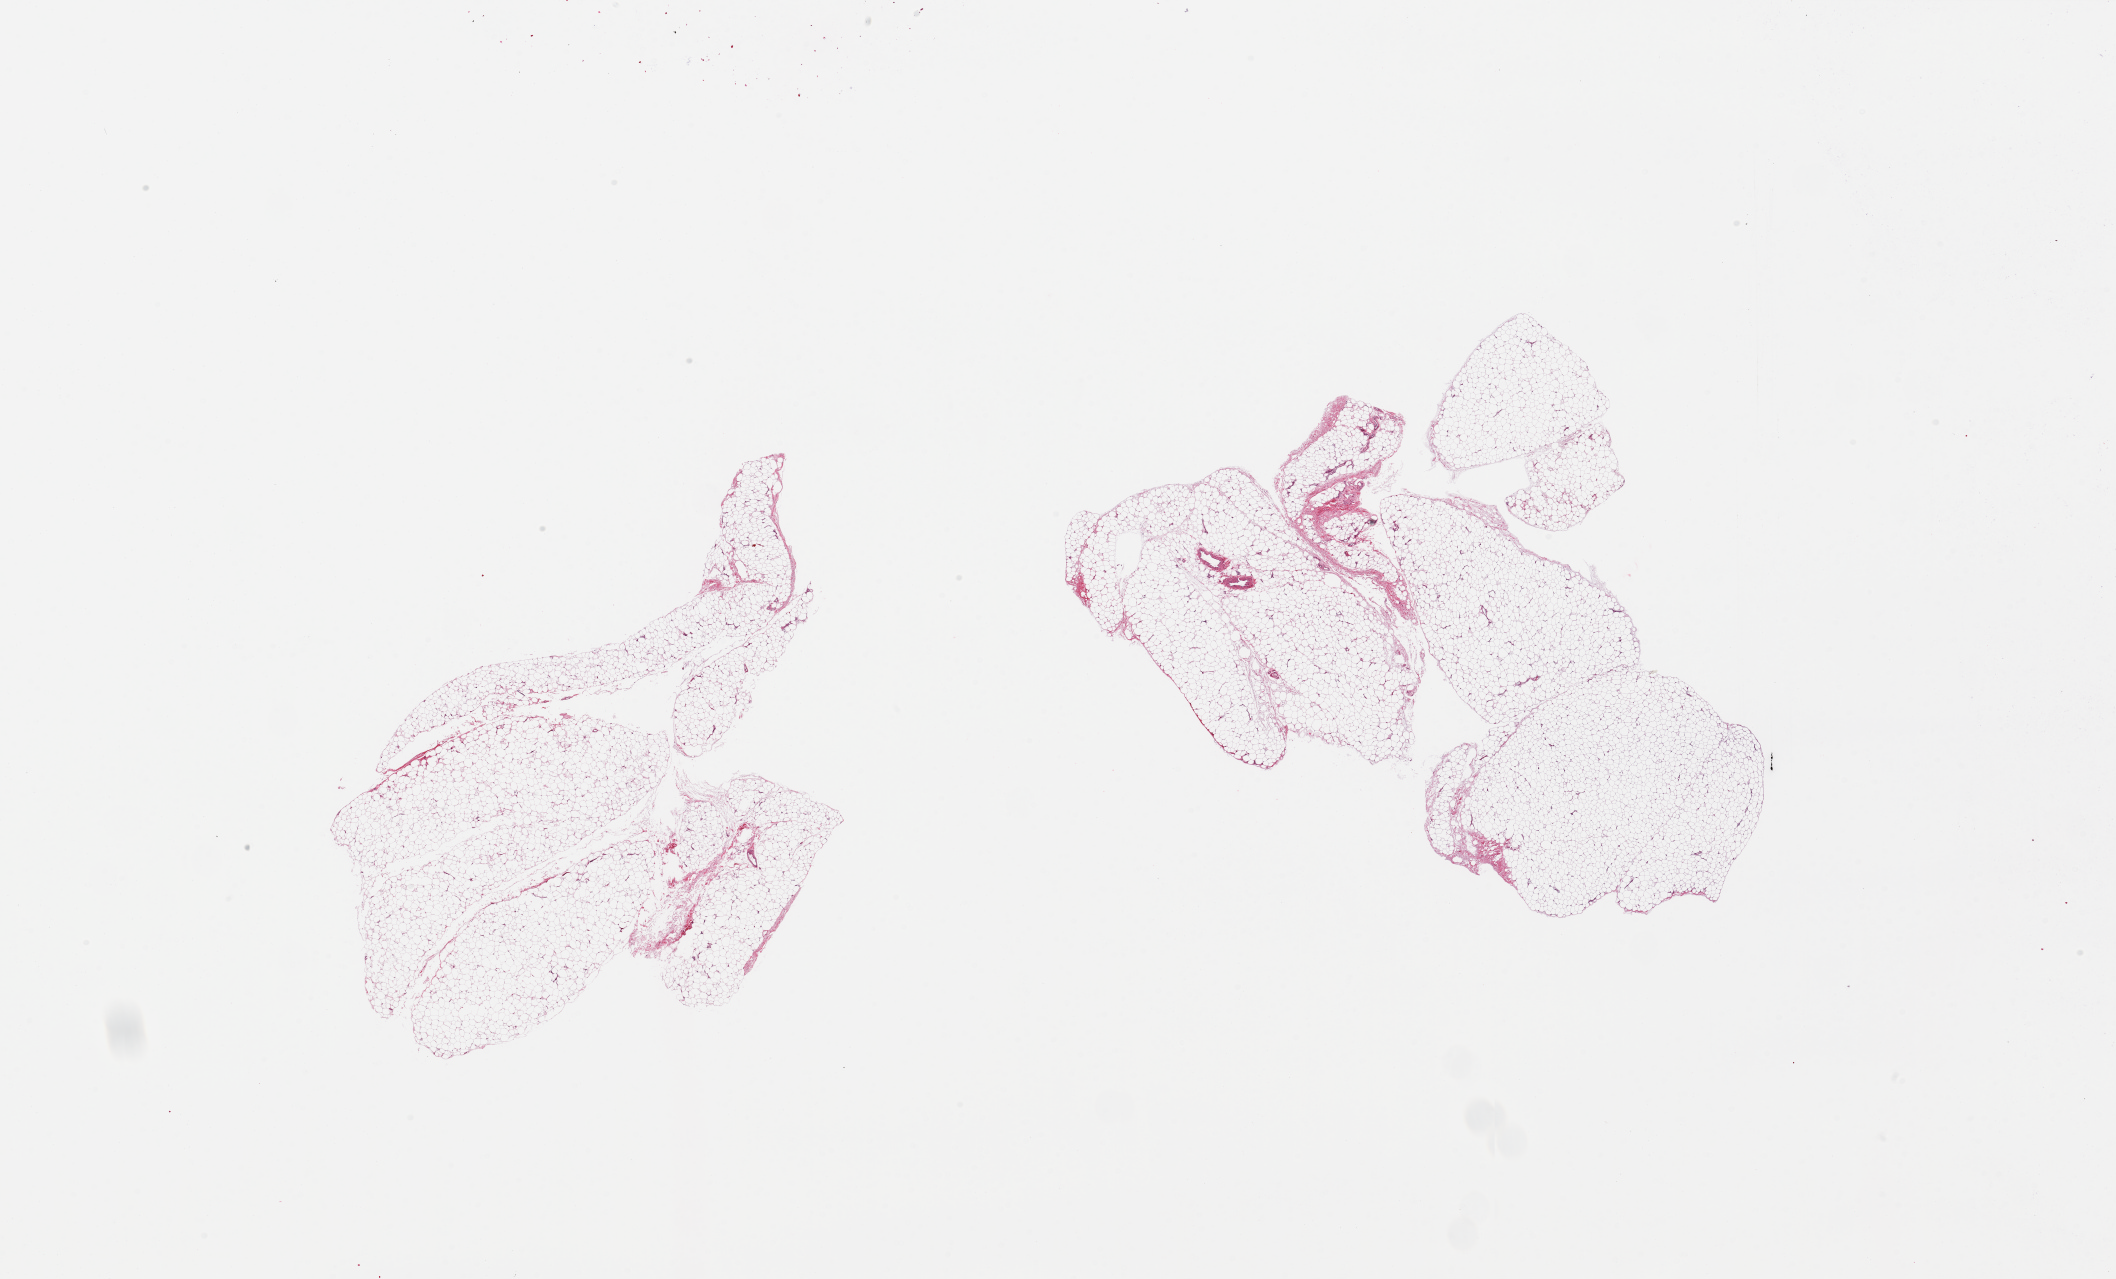
Haematoxylin and eosin whole-slide image, shown as a low-resolution overview of the whole scanned area (about 33.5 x 20.2 mm); PAXgene-fixed, paraffin-embedded tissue; section of adipose tissue (target tissue); tissue donor sample. Donor: male.
- pathologist's review note for this sample: 2 pieces; fascia/vascular elements are ~5-10% tissue